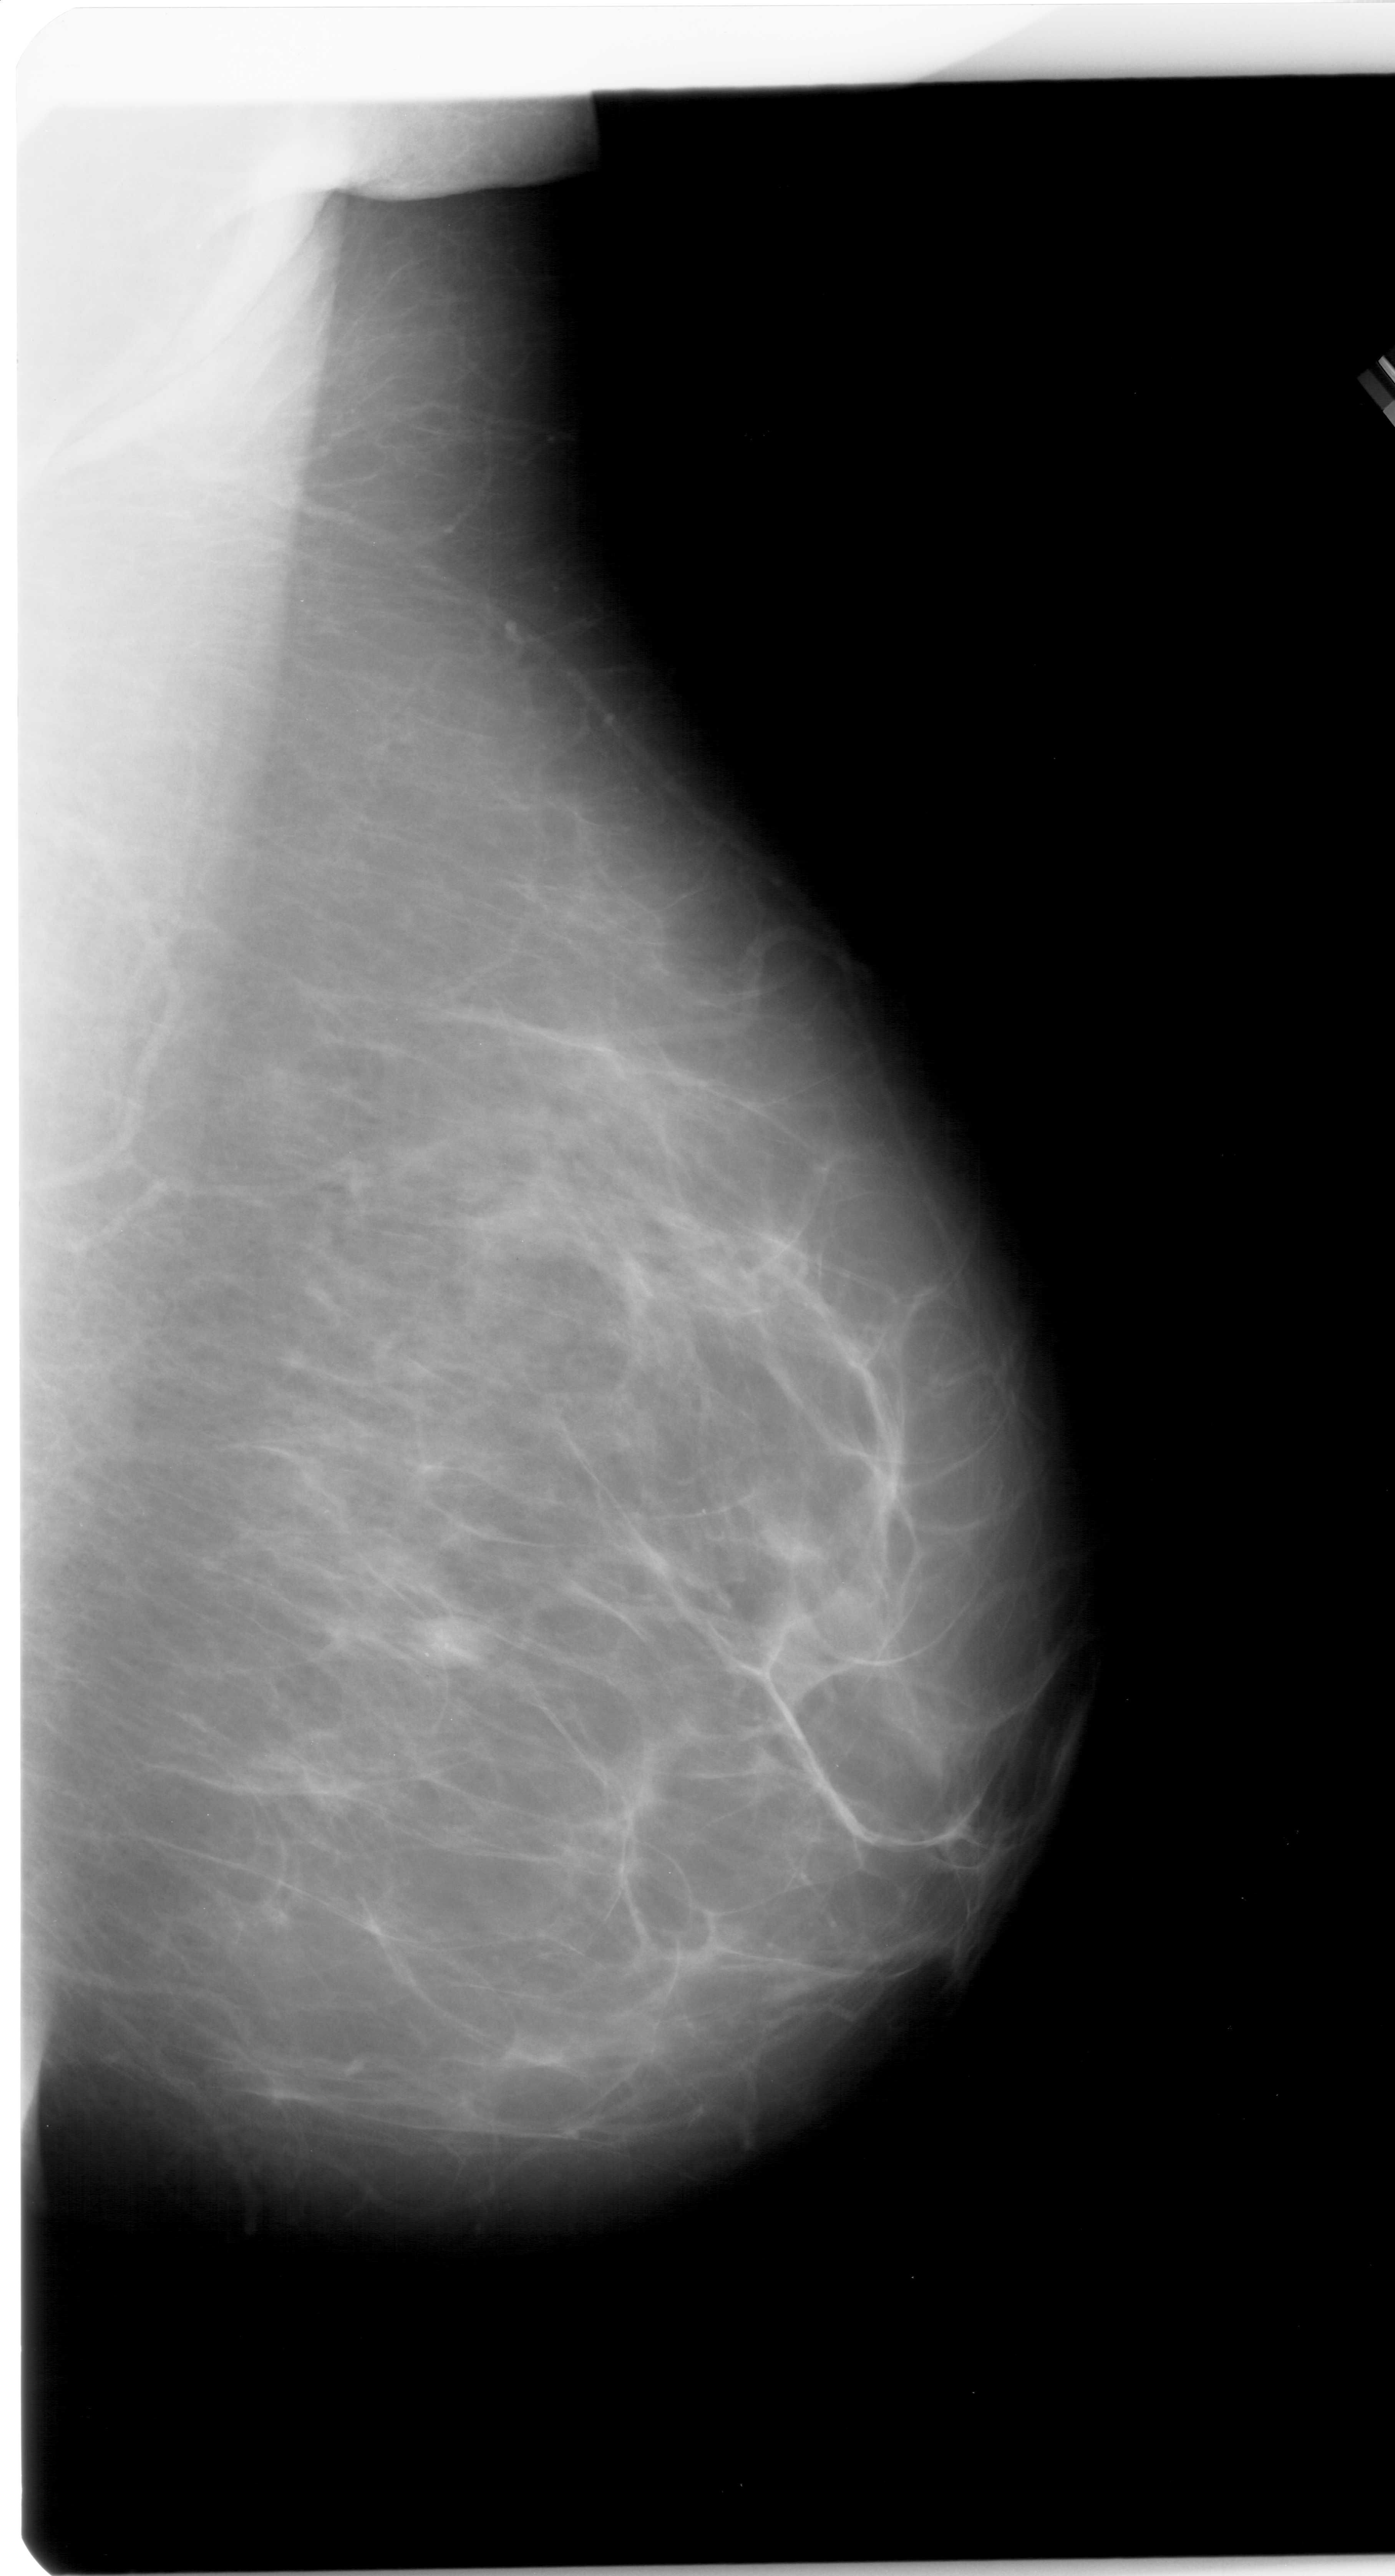
Mammogram (digitized film). Right breast. MLO view. 1395 × 2576 image matrix.
Expert-marked regions of interest on this film, with their recorded descriptors:
- mass, shape oval, margins circumscribed; BI-RADS assessment category 3; subtlety rating 4 on a 1 (subtle) to 5 (obvious) scale; pathology (as recorded): benign: bounding box (x1, y1, x2, y2) in pixels: (404, 1596, 496, 1672)